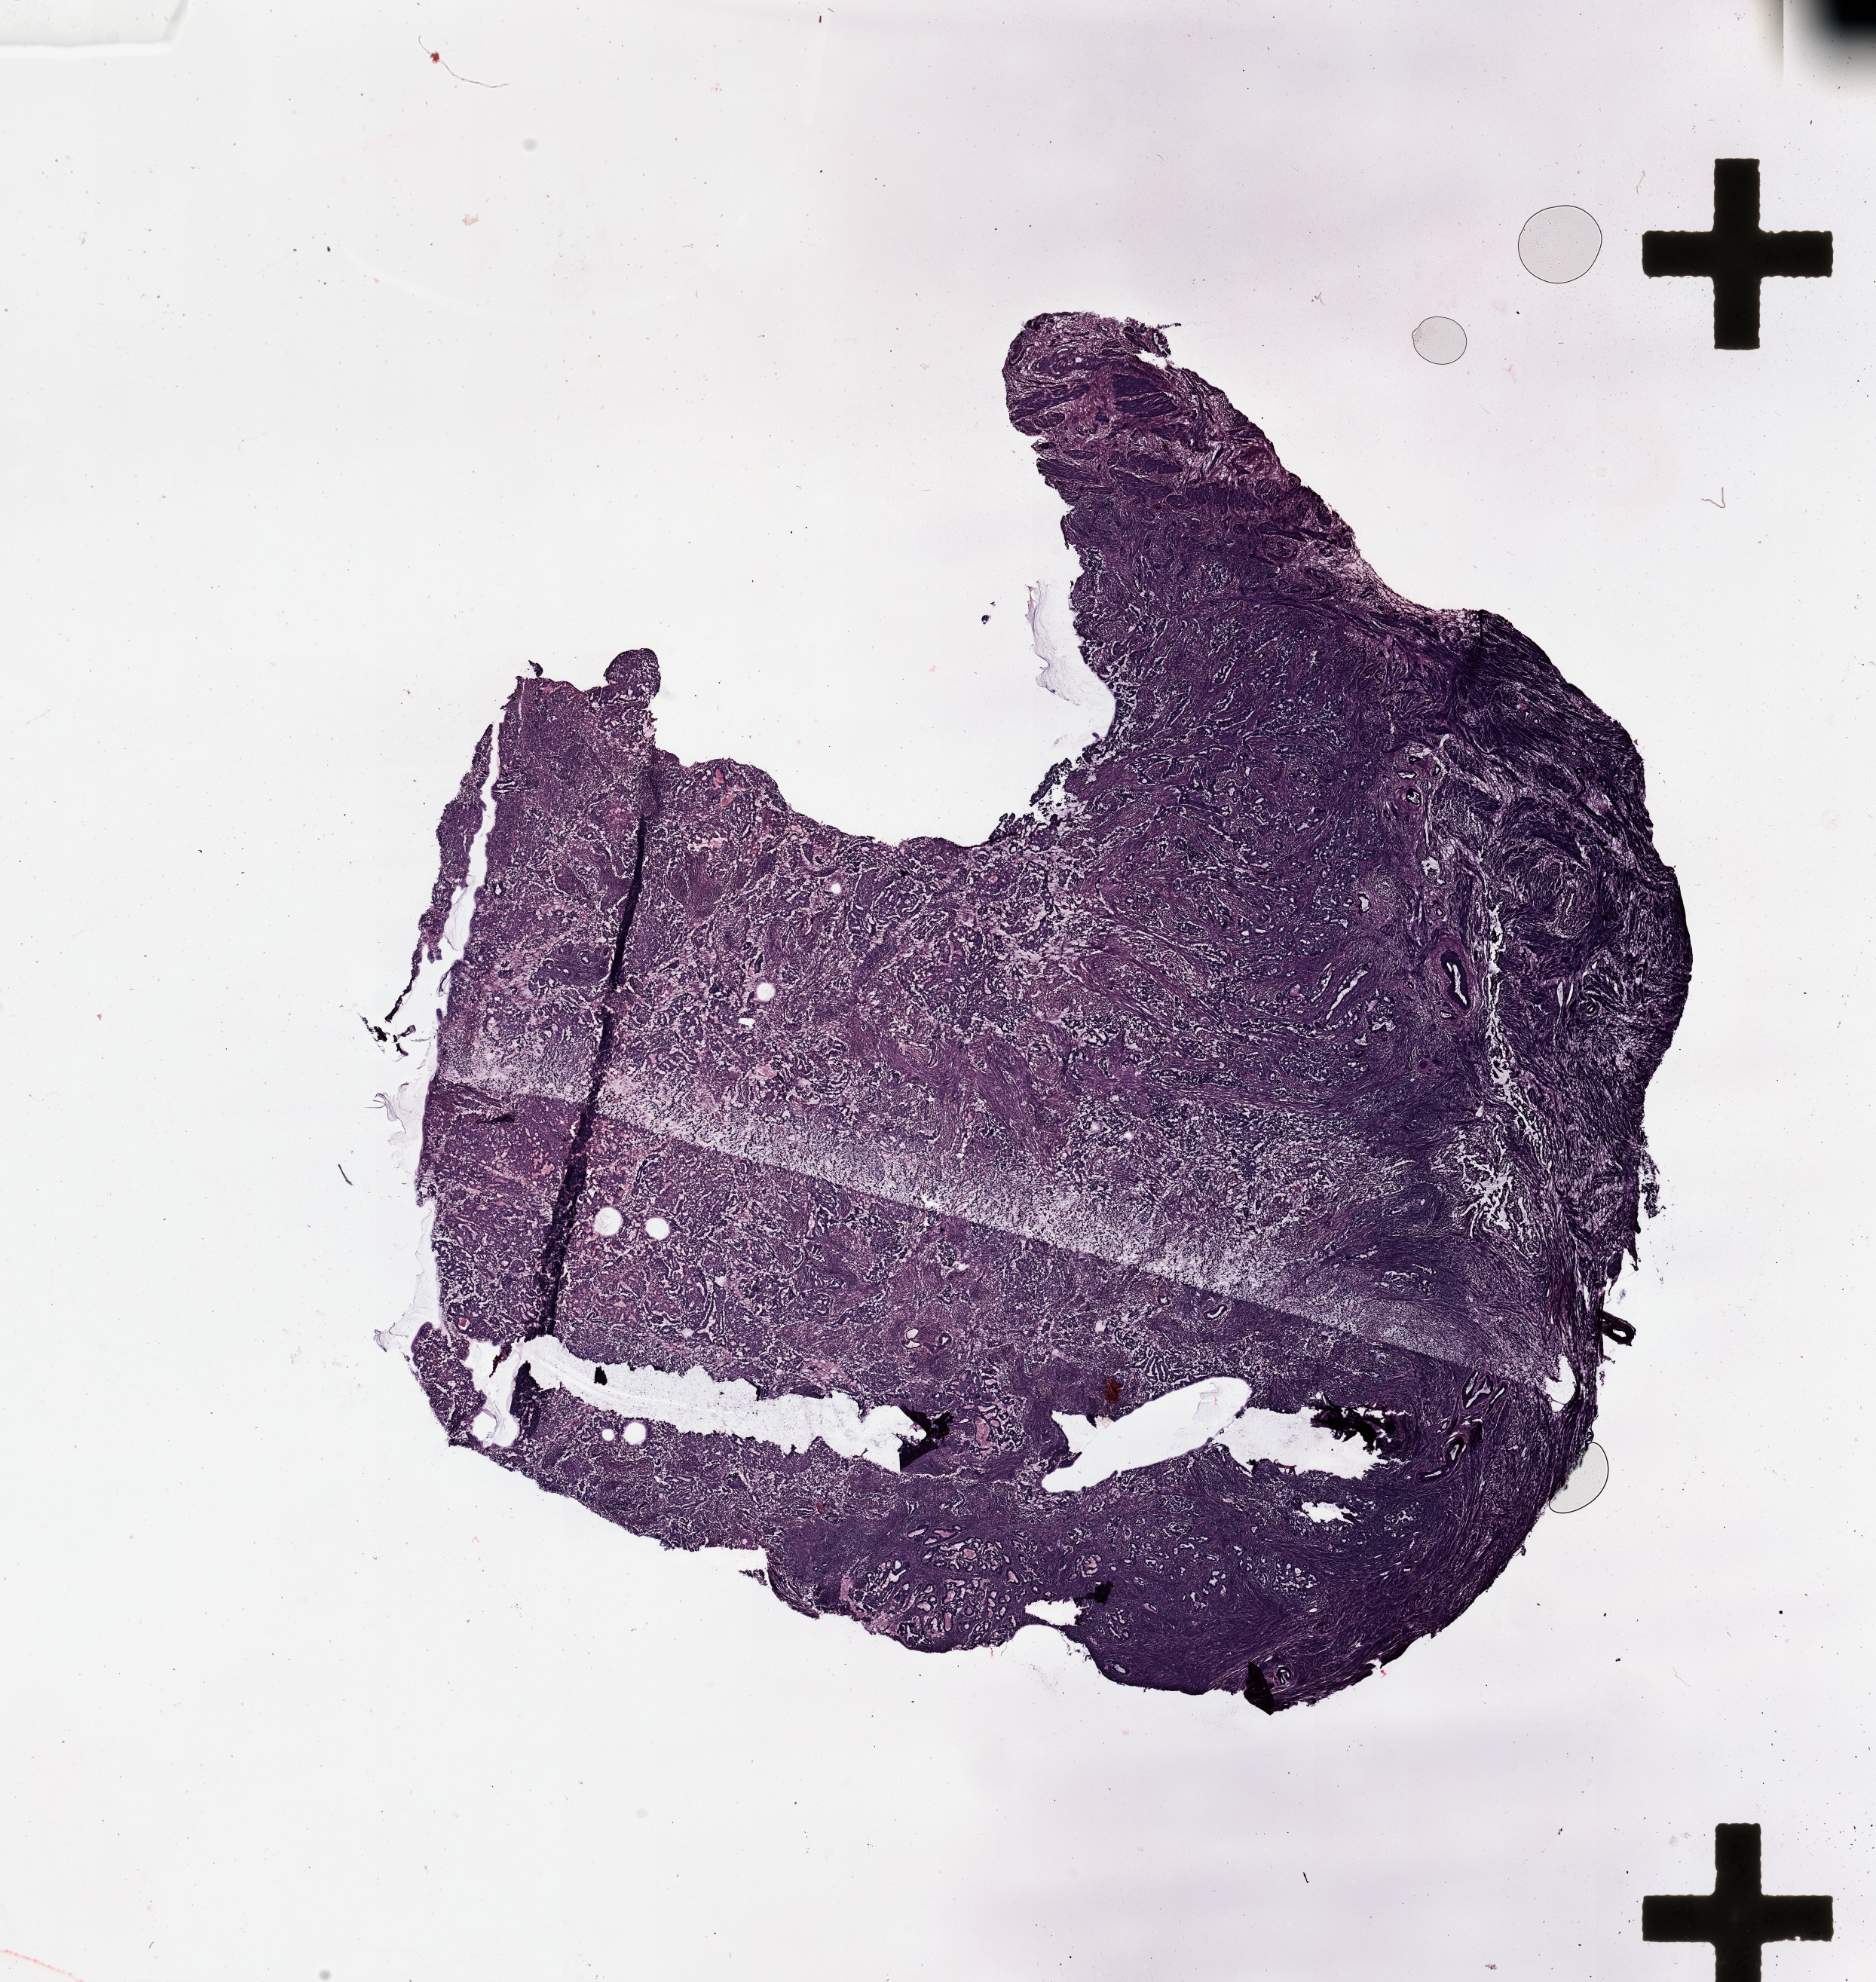
Digitized Hematoxylin and eosin (H&E) stained tissue section (whole slide), a low-resolution overview of the entire scanned area, about 19.7 x 20.8 mm (slide scanned at 20x), uterus, tumour tissue. Female, 62 y/o. Histologic grade: G2 (moderately differentiated).
AJCC pathologic stage: I. Histologic diagnosis: Endometrioid adenocarcinoma, NOS.